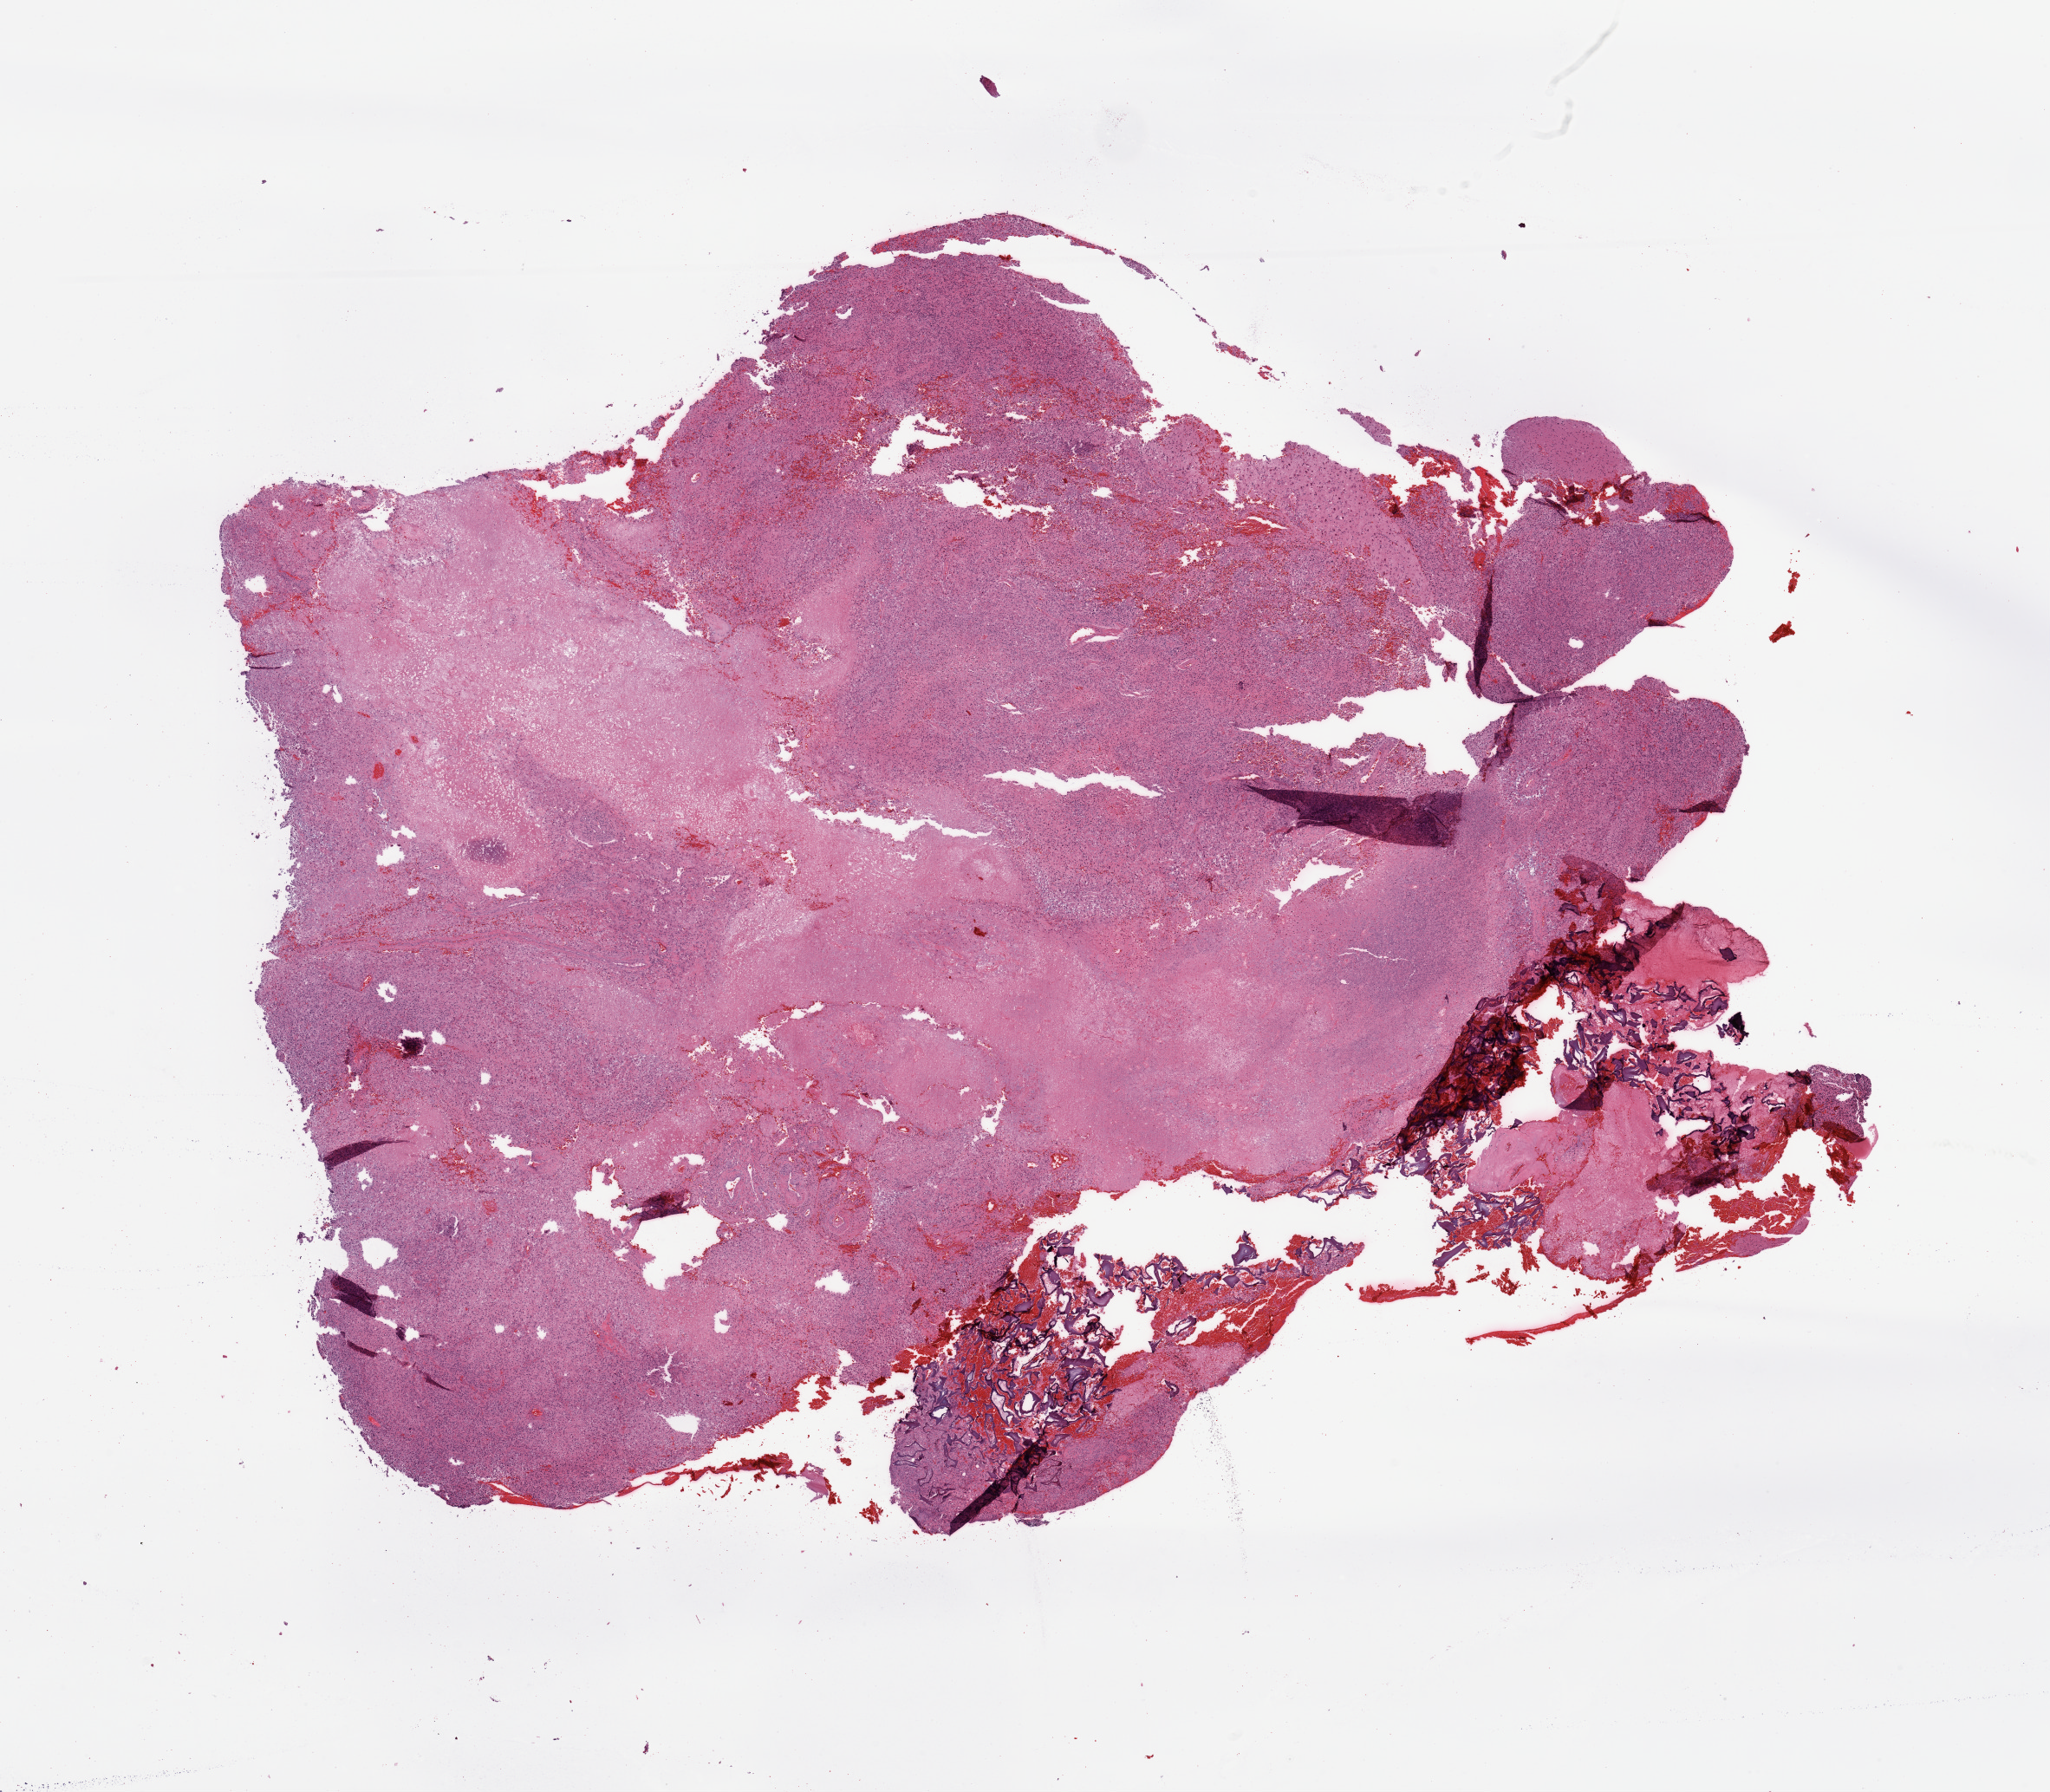
Whole-slide histology image, H&E — a low-resolution overview of the entire scanned area, about 18.7 x 16.3 mm (acquisition: 20x scan), tumour tissue sample, brain. 60-year-old male patient.
Diagnosis: Glioblastoma. Primary tumour site (as recorded): frontal lobe.